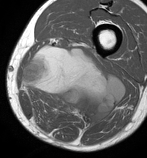
MRI of an extremity soft-tissue mass, one axial slice; slice 38 of 86 in the series (ordered by position); MR volume resampled by the dataset authors to the PET/CT grid (not the native acquisition matrix); 3.27 mm slice thickness; 147 × 158 image matrix. Male patient. From the clinical record (not read from this slice): histological type: undifferentiated pleomorphic liposarcoma; grade: high; site of the primary tumour: left thigh.
Outlined on this slice (expert contour drawn on MRI and transferred to this co-registered scan by the dataset authors):
- gross tumour volume including surrounding oedema: bounding box [x1, y1, x2, y2] px = [23, 44, 125, 127]
- gross tumour volume (mass): [23, 46, 125, 127]